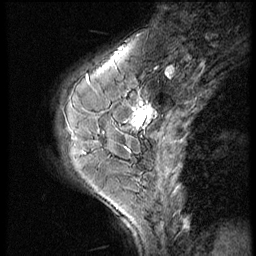
Breast MRI (dynamic contrast-enhanced), one sagittal slice; position 19 of 56 along the scan axis; 3 images stored at this slice position (order not interpretable as contrast timing); 1.5 T; TE 4.2 ms, TR 9 ms; 2.5 mm slice thickness; 256 × 256 image matrix. Female patient, age 46 years. Case-level facts recorded for this patient, not image findings: setting: breast cancer imaged before/during neoadjuvant chemotherapy; receptor status: HER2-positive.
Outlined on this slice (semi-automatically segmented with operator editing):
- analysis volume of interest (the breast-tissue region the enhancement analysis was run in; not a lesion): bounding box <73,86,164,161> (left, top, right, bottom; pixels)
- tumour enhancement mask (voxels above the 140 % enhancement threshold inside the analysis volume of interest): <133,101,154,130>